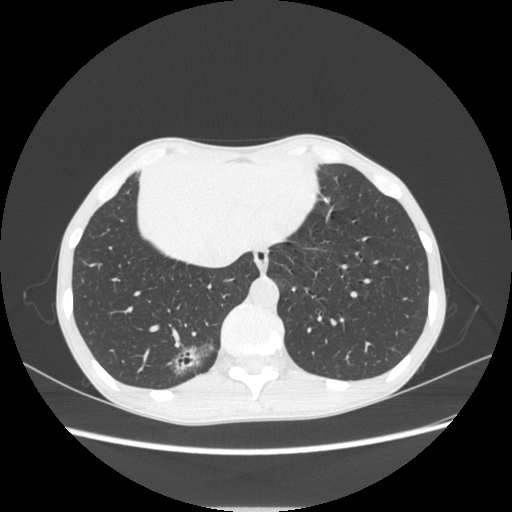
Chest CT, one axial slice. Position 67 of 272 along the scan axis. Reconstruction kernel STANDARD. Lung window (W 1500 / L -600 HU). 1.25 mm slice thickness. 512 × 512 image matrix. Female patient, age 51 years. Case-level facts recorded for this patient, not image findings: clinical TNM (as recorded): T1c N0 M0; histopathological grade: G2-3.
Structures marked on this image (rectangle marked by the reading radiologist):
- lung tumour (recorded histology: adenocarcinoma): bounding box <163,332,216,380> (left, top, right, bottom; pixels)